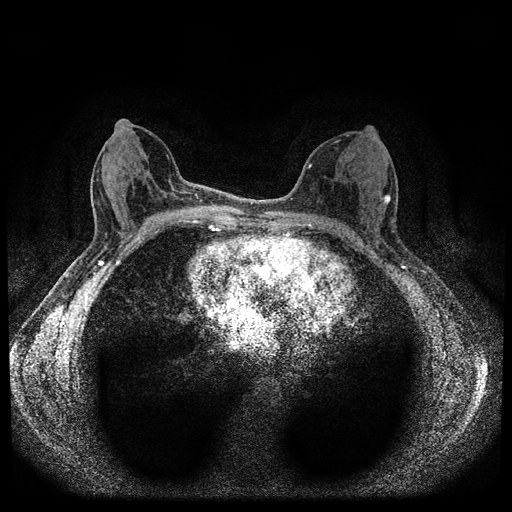
Breast MRI (dynamic contrast-enhanced, multi-phase), one axial slice; slice 46 of 112 in the series (ordered by position); dynamic contrast-enhanced series, time point 2 of 5 at this slice position (early post-contrast); 1.5 T; TE 2.7 ms, TR 5.4 ms; 512 × 512 image matrix, field of view 320 × 320 mm. Female patient, age 61 years.
Outlined on this slice (semi-automatically segmented with operator editing):
- breast lesion (labelled 'tumour' in the annotation; benign lesions carry a separate 'benign' label): bounding box (x1, y1, x2, y2) in pixels: (383, 194, 391, 204)